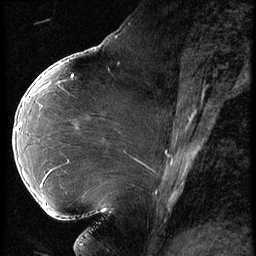
Breast MRI (dynamic contrast-enhanced), one sagittal slice; slice 28 of 62 in the series (ordered by position); 3 images stored at this slice position (order not interpretable as contrast timing); 1.5 T; TE 4.2 ms, TR 9 ms; 2.5 mm slice thickness; 256 × 256 image matrix, field of view 180 × 180 mm. Patient: female, 43 years. Case-level facts recorded for this patient, not image findings: setting: breast cancer imaged before/during neoadjuvant chemotherapy; receptor status: HER2-positive.
Structures marked on this image (semi-automatically segmented with operator editing):
- analysis volume of interest (the breast-tissue region the enhancement analysis was run in; not a lesion): bounding box [x1, y1, x2, y2] px = [13, 90, 82, 203]
- tumour enhancement mask (voxels above the 140 % enhancement threshold inside the analysis volume of interest): [17, 126, 20, 130]